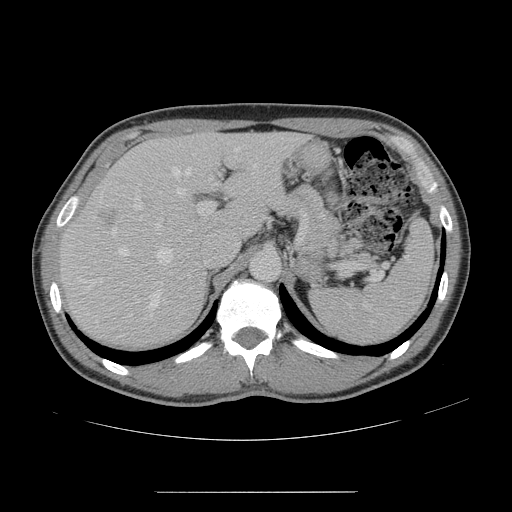
Contrast-enhanced abdominal CT, one axial slice; 120 kVp; intravenous contrast given; soft-tissue window (W 400 / L 40 HU); 512 × 512 image matrix, field of view 401 × 401 mm. Male patient, age 53 years. Case-level facts recorded for this patient, not image findings: diagnosis: colorectal cancer liver metastases, imaged before liver resection; multiple liver metastases: yes; largest metastasis: 2.4 cm; chemotherapy before resection: yes.
Annotated regions visible in this slice (expert manual segmentation):
- hepatic veins: bounding box (x1, y1, x2, y2) in pixels: (88, 147, 255, 310)
- liver: (62, 134, 302, 345)
- planned liver remnant (the part of the liver to remain after resection): (148, 135, 302, 234)
- portal vein (with intrahepatic branches): (132, 191, 213, 234)
- liver metastasis: (100, 209, 121, 228)